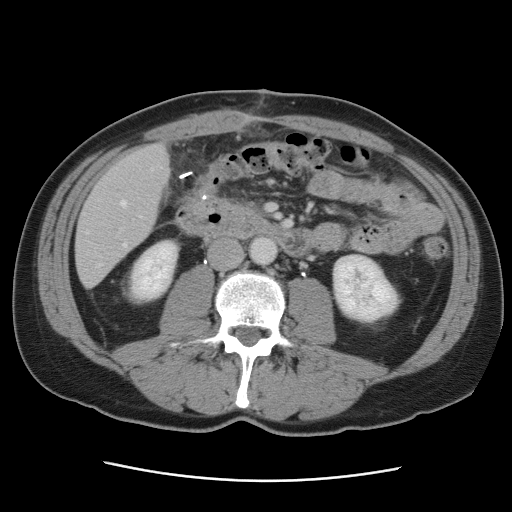
Contrast-enhanced abdominal CT, one axial slice. Slice 22 of 89 in the series (ordered by position). Intravenous contrast given. Soft-tissue window (W 400 / L 40 HU). 512 × 512 image matrix, field of view 366 × 366 mm. Male patient, age 59 years. From the clinical record (not read from this slice): diagnosis: colorectal cancer liver metastases, imaged before liver resection; multiple liver metastases: yes; largest metastasis: 0.6 cm; disease in both lobes: yes.
Outlined on this slice (outlined manually by an expert reader):
- hepatic veins: box from (x=86, y=168) to (x=153, y=267) px
- liver: (x=77, y=145)–(x=169, y=286)
- planned liver remnant (the part of the liver to remain after resection): (x=77, y=145)–(x=169, y=252)